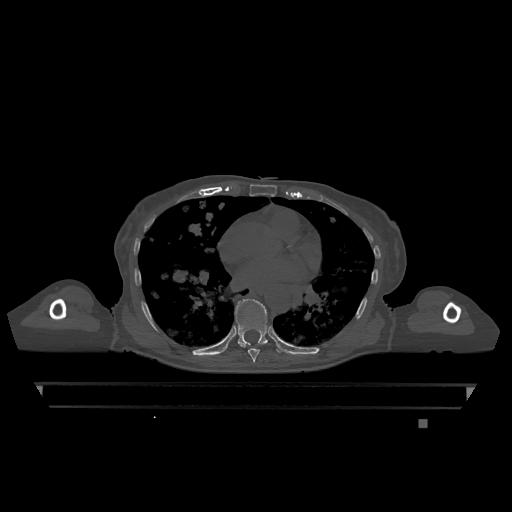
CT including the spine, one axial slice; position 712 of 1317 along the scan axis; bone window (W 1800 / L 400 HU); 0.5 mm slice thickness; 512 × 512 image matrix, field of view 500 × 500 mm. Female patient, age 74 years. Case-level facts recorded for this patient, not image findings: primary cancer: lung.
Outlined on this slice (semi-automatically segmented with operator editing):
- T7 vertebra: box from (x=239, y=344) to (x=260, y=362) px
- T9 vertebra: (x=235, y=298)–(x=281, y=353)